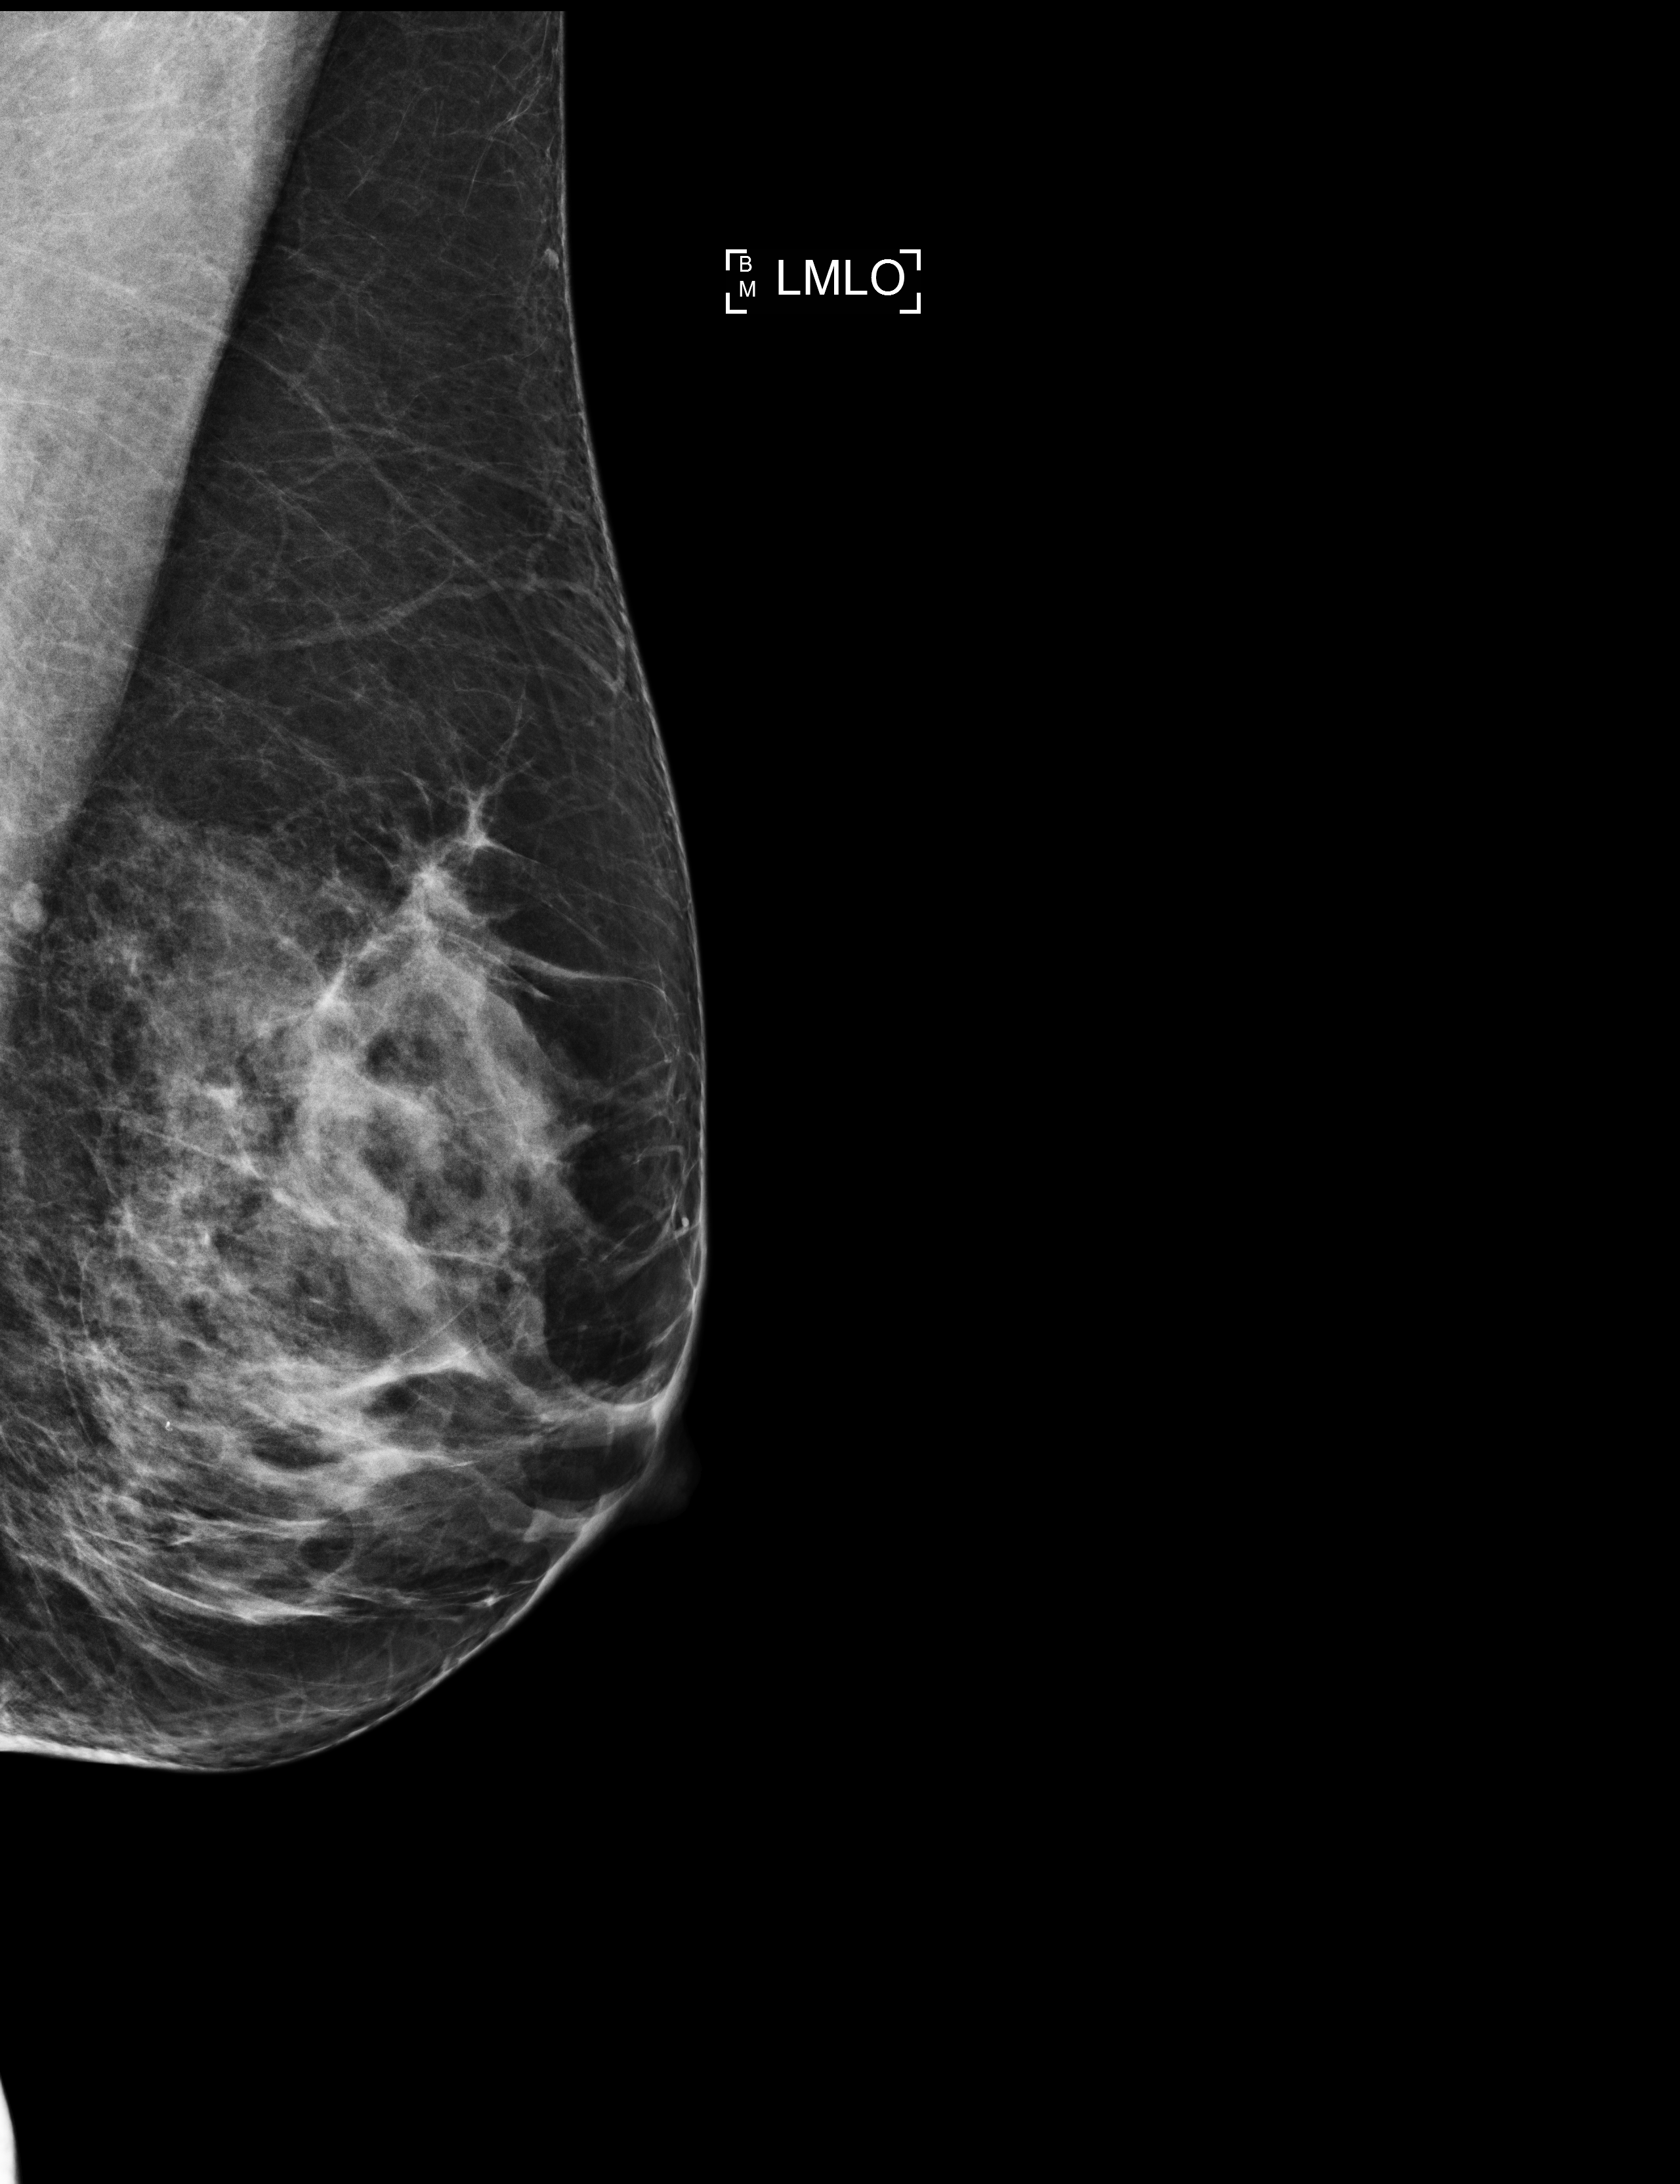
Screening examination; system: Selenia Dimensions. Female patient, age 60 years.
Image type: full-field digital mammogram. Breast: left. Projection: medio-lateral oblique projection.